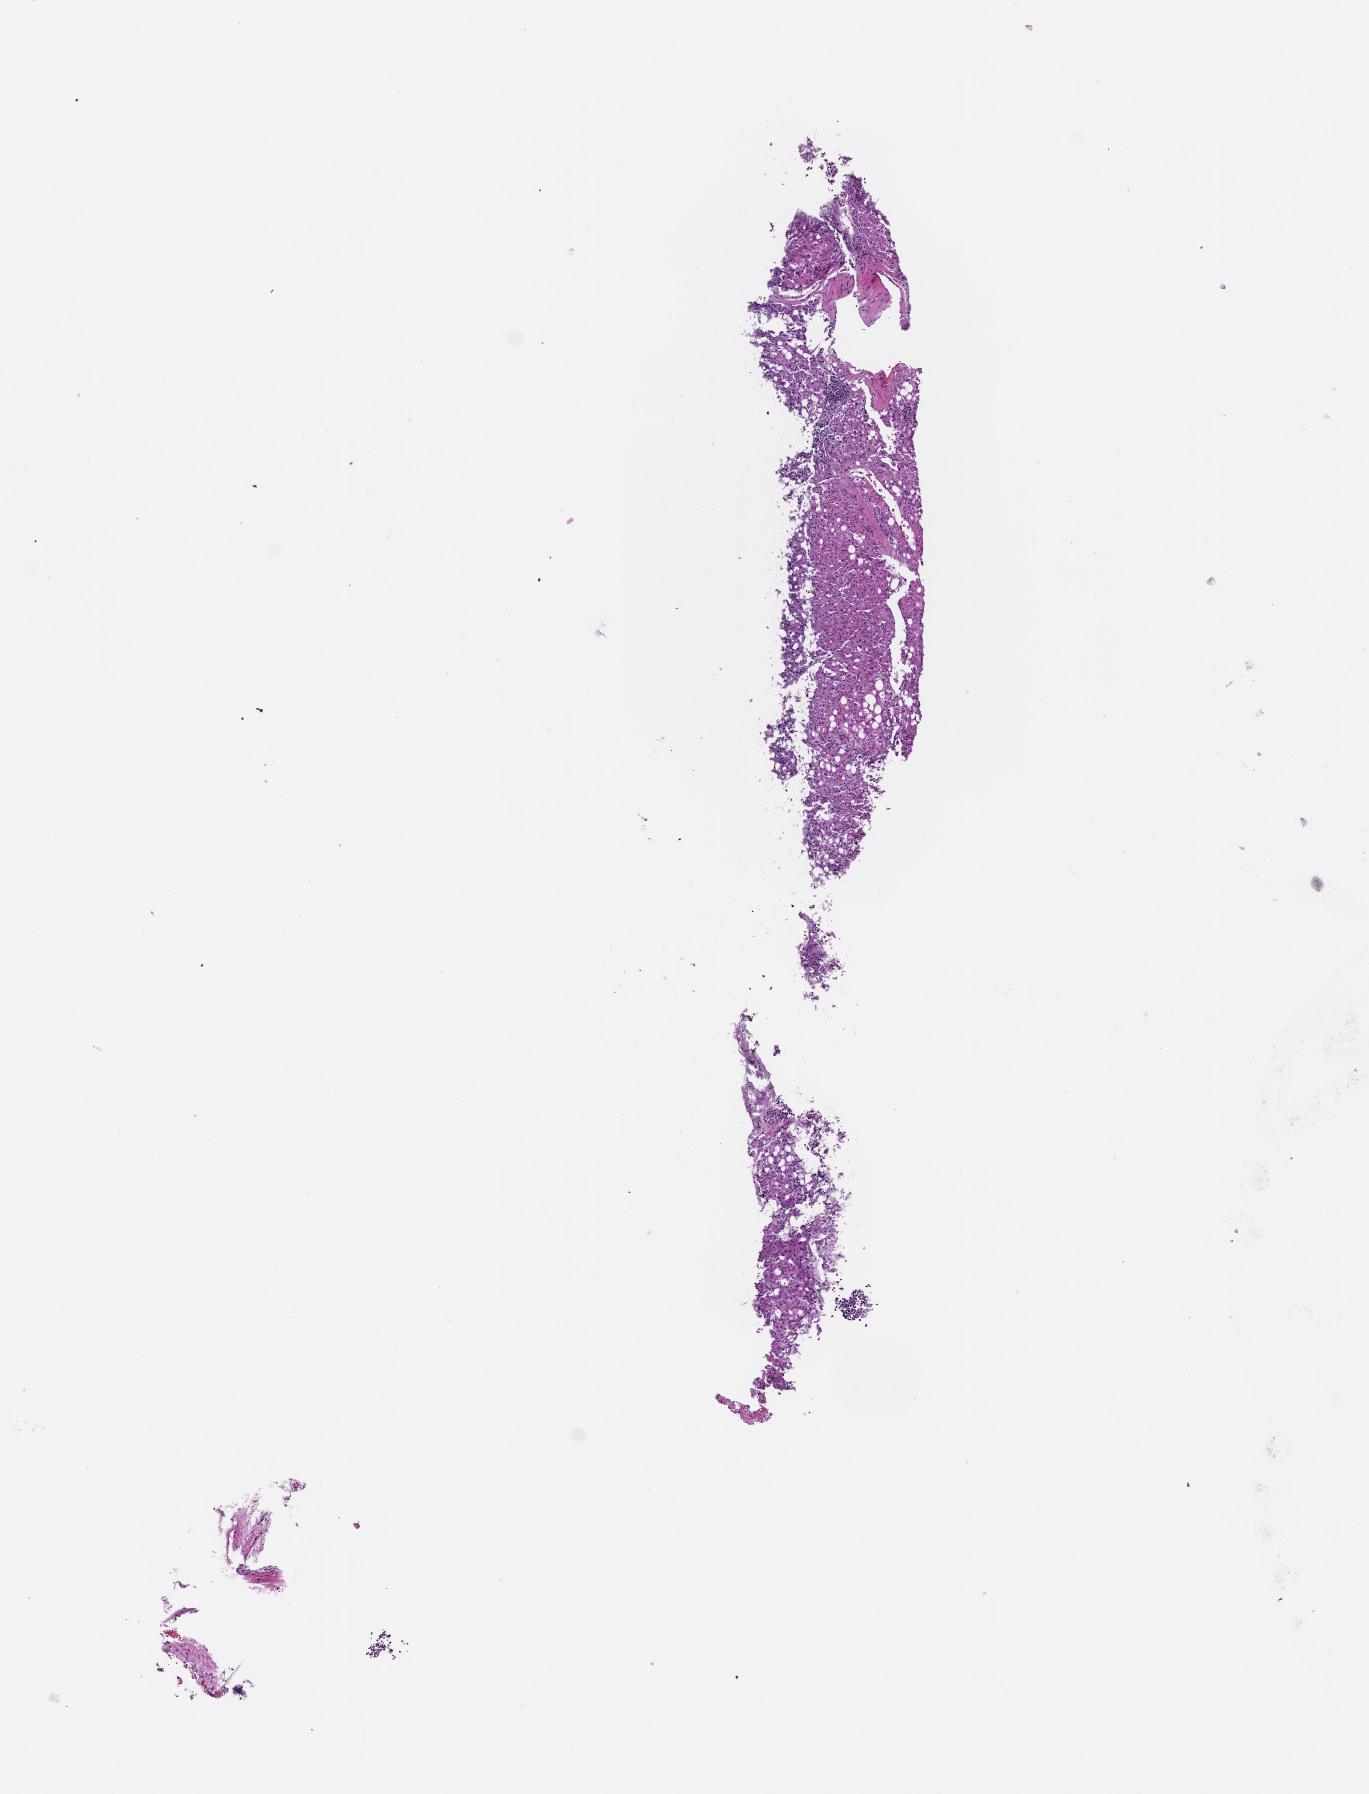
H&E whole-slide image — low-resolution overview of the scanned area, about 5.5 x 7.2 mm, formalin-fixed, paraffin-embedded (FFPE) tissue. Patient: male.
This section: metastasis (sampled organ not recorded). Patient diagnosis (primary): Melanoma.